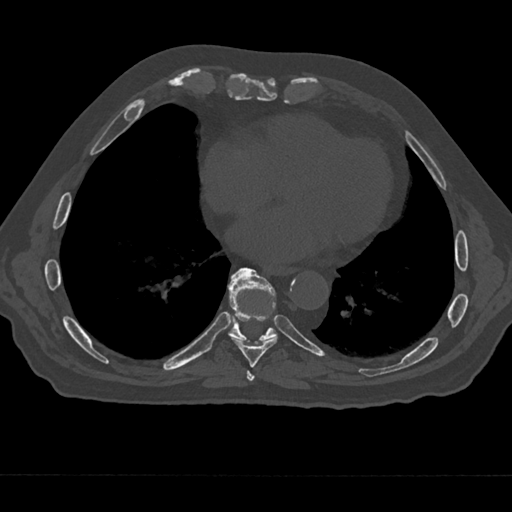
CT including the spine, one axial slice; position 293 of 797 along the scan axis; reconstruction kernel Br40s/3; 120 kVp; bone window (W 1800 / L 400 HU); 0.5 mm slice thickness; 512 × 512 image matrix, field of view 377 × 377 mm. Male patient, age 75 years. Case-level facts recorded for this patient, not image findings: primary cancer: renal; vertebrae with lytic lesions (as recorded): T4.
Annotated regions visible in this slice (semi-automatically segmented with operator editing):
- T7 vertebra: bounding box (x1, y1, x2, y2) in pixels: (244, 370, 258, 385)
- T8 vertebra: (232, 285, 278, 368)
- T9 vertebra: (228, 267, 277, 342)